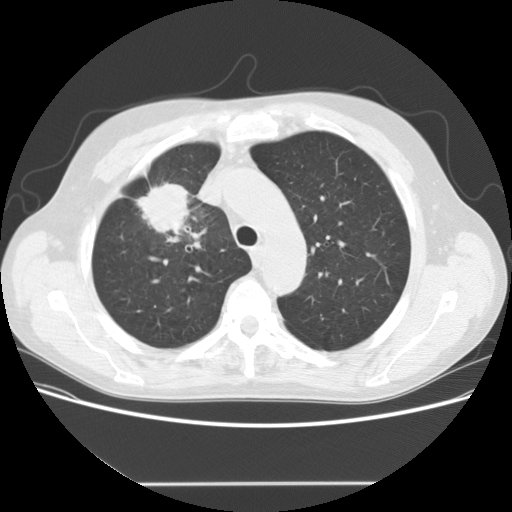
Low-dose screening chest CT, one axial slice. Position 116 of 153 along the scan axis. 120 kVp. Lung window (W 1500 / L -600 HU). 512 × 512 image matrix.
Structures marked on this image (expert manual segmentation):
- lesion 1 (tumor, upper lobe of right lung): box from (x=137, y=183) to (x=191, y=243) px